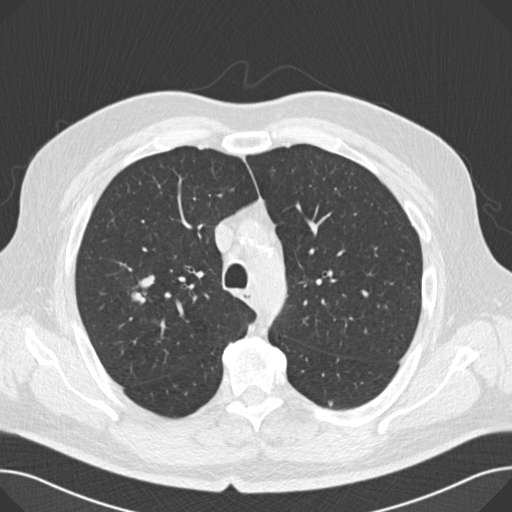
Chest CT (low-dose screening protocol), one axial image, second annual screen, lung window (W 1500 / L -600 HU), 120 kVp. Male, age 67 years at enrolment. Current smoker at enrolment.
Lesion marked by an expert reader, bounding box <118,269,166,313> (left, top, right, bottom; pixels). Screening reader's record for this exam: no non-calcified nodule ≥4 mm recorded. Official screen result: negative screen, significant abnormalities not suspicious for lung cancer. Lung cancer was diagnosed 194 days after this screen: small cell carcinoma, NOS, right middle lobe, stage IA (AJCC 6th edition), 20 mm at pathology.